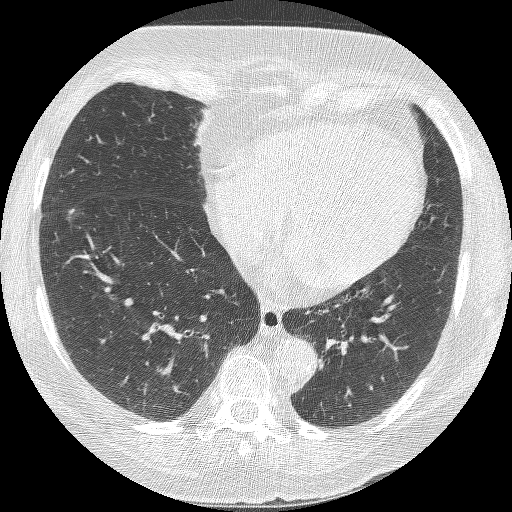
Axial slice from a low-dose chest CT screening exam; second screening round (one year after baseline); lung window (W 1500 / L -600 HU); lung (sharp) reconstruction kernel (BONE). Female, age 68 years at enrolment. Current smoker at enrolment.
- Expert-annotated lung lesion, box from (x=33, y=194) to (x=95, y=253) px.
- The exam's reader record, not a measurement of the box and not confirmed to be the same lesion: non-calcified nodule or mass ≥4 mm, right lower lobe, 18 × 15 mm, poorly defined margins, ground glass attenuation, pre-existing on the prior screen: yes; interval growth: yes.
- Later outcome: lung cancer diagnosed 42 days after this screen — bronchiolo-alveolar adenocarcinoma, NOS, right lower lobe, well differentiated (G1), stage IA (AJCC 6th edition), 13 mm at pathology.